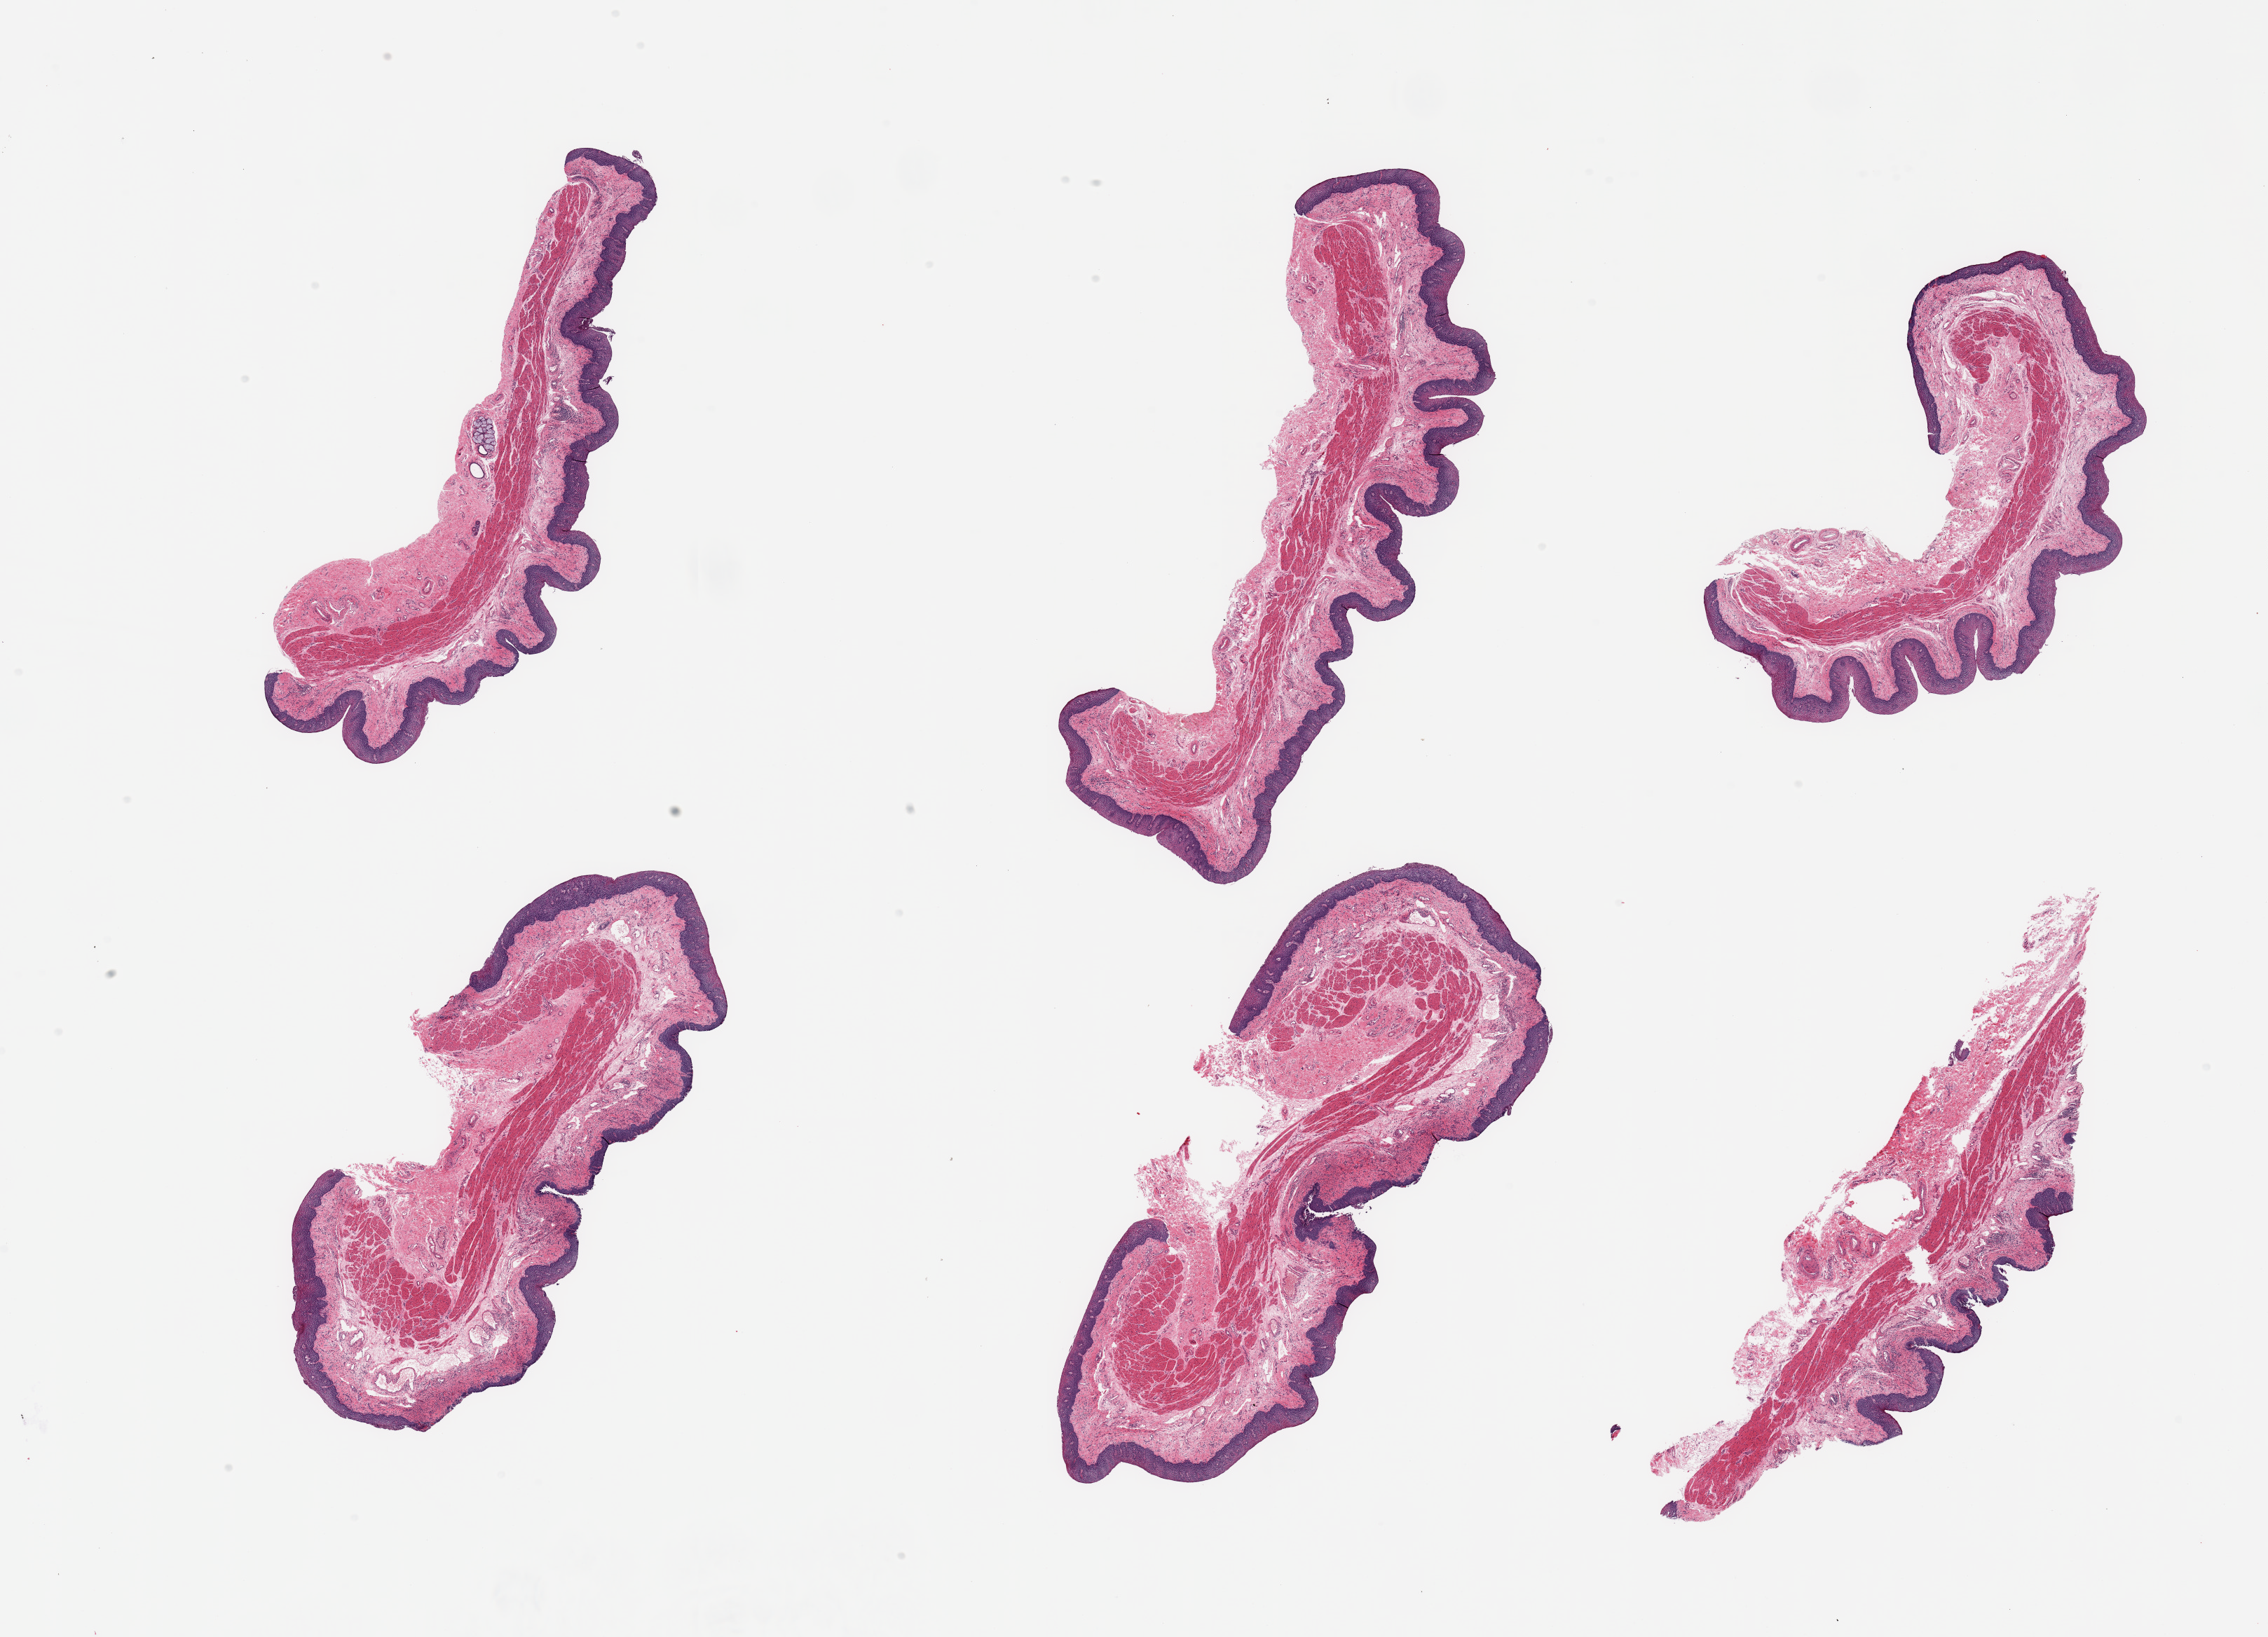
Digitized hematoxylin and eosin (H&E)-stained section, low-resolution overview of the scanned area, about 25.6 x 18.5 mm; PAXgene-fixed paraffin-embedded (PFPE) section; sampled site (target tissue): esophageal mucous membrane; donor tissue sample. Donor: female.
Pathologist's review note for this sample: 6 pieces; erosive esophagitis.